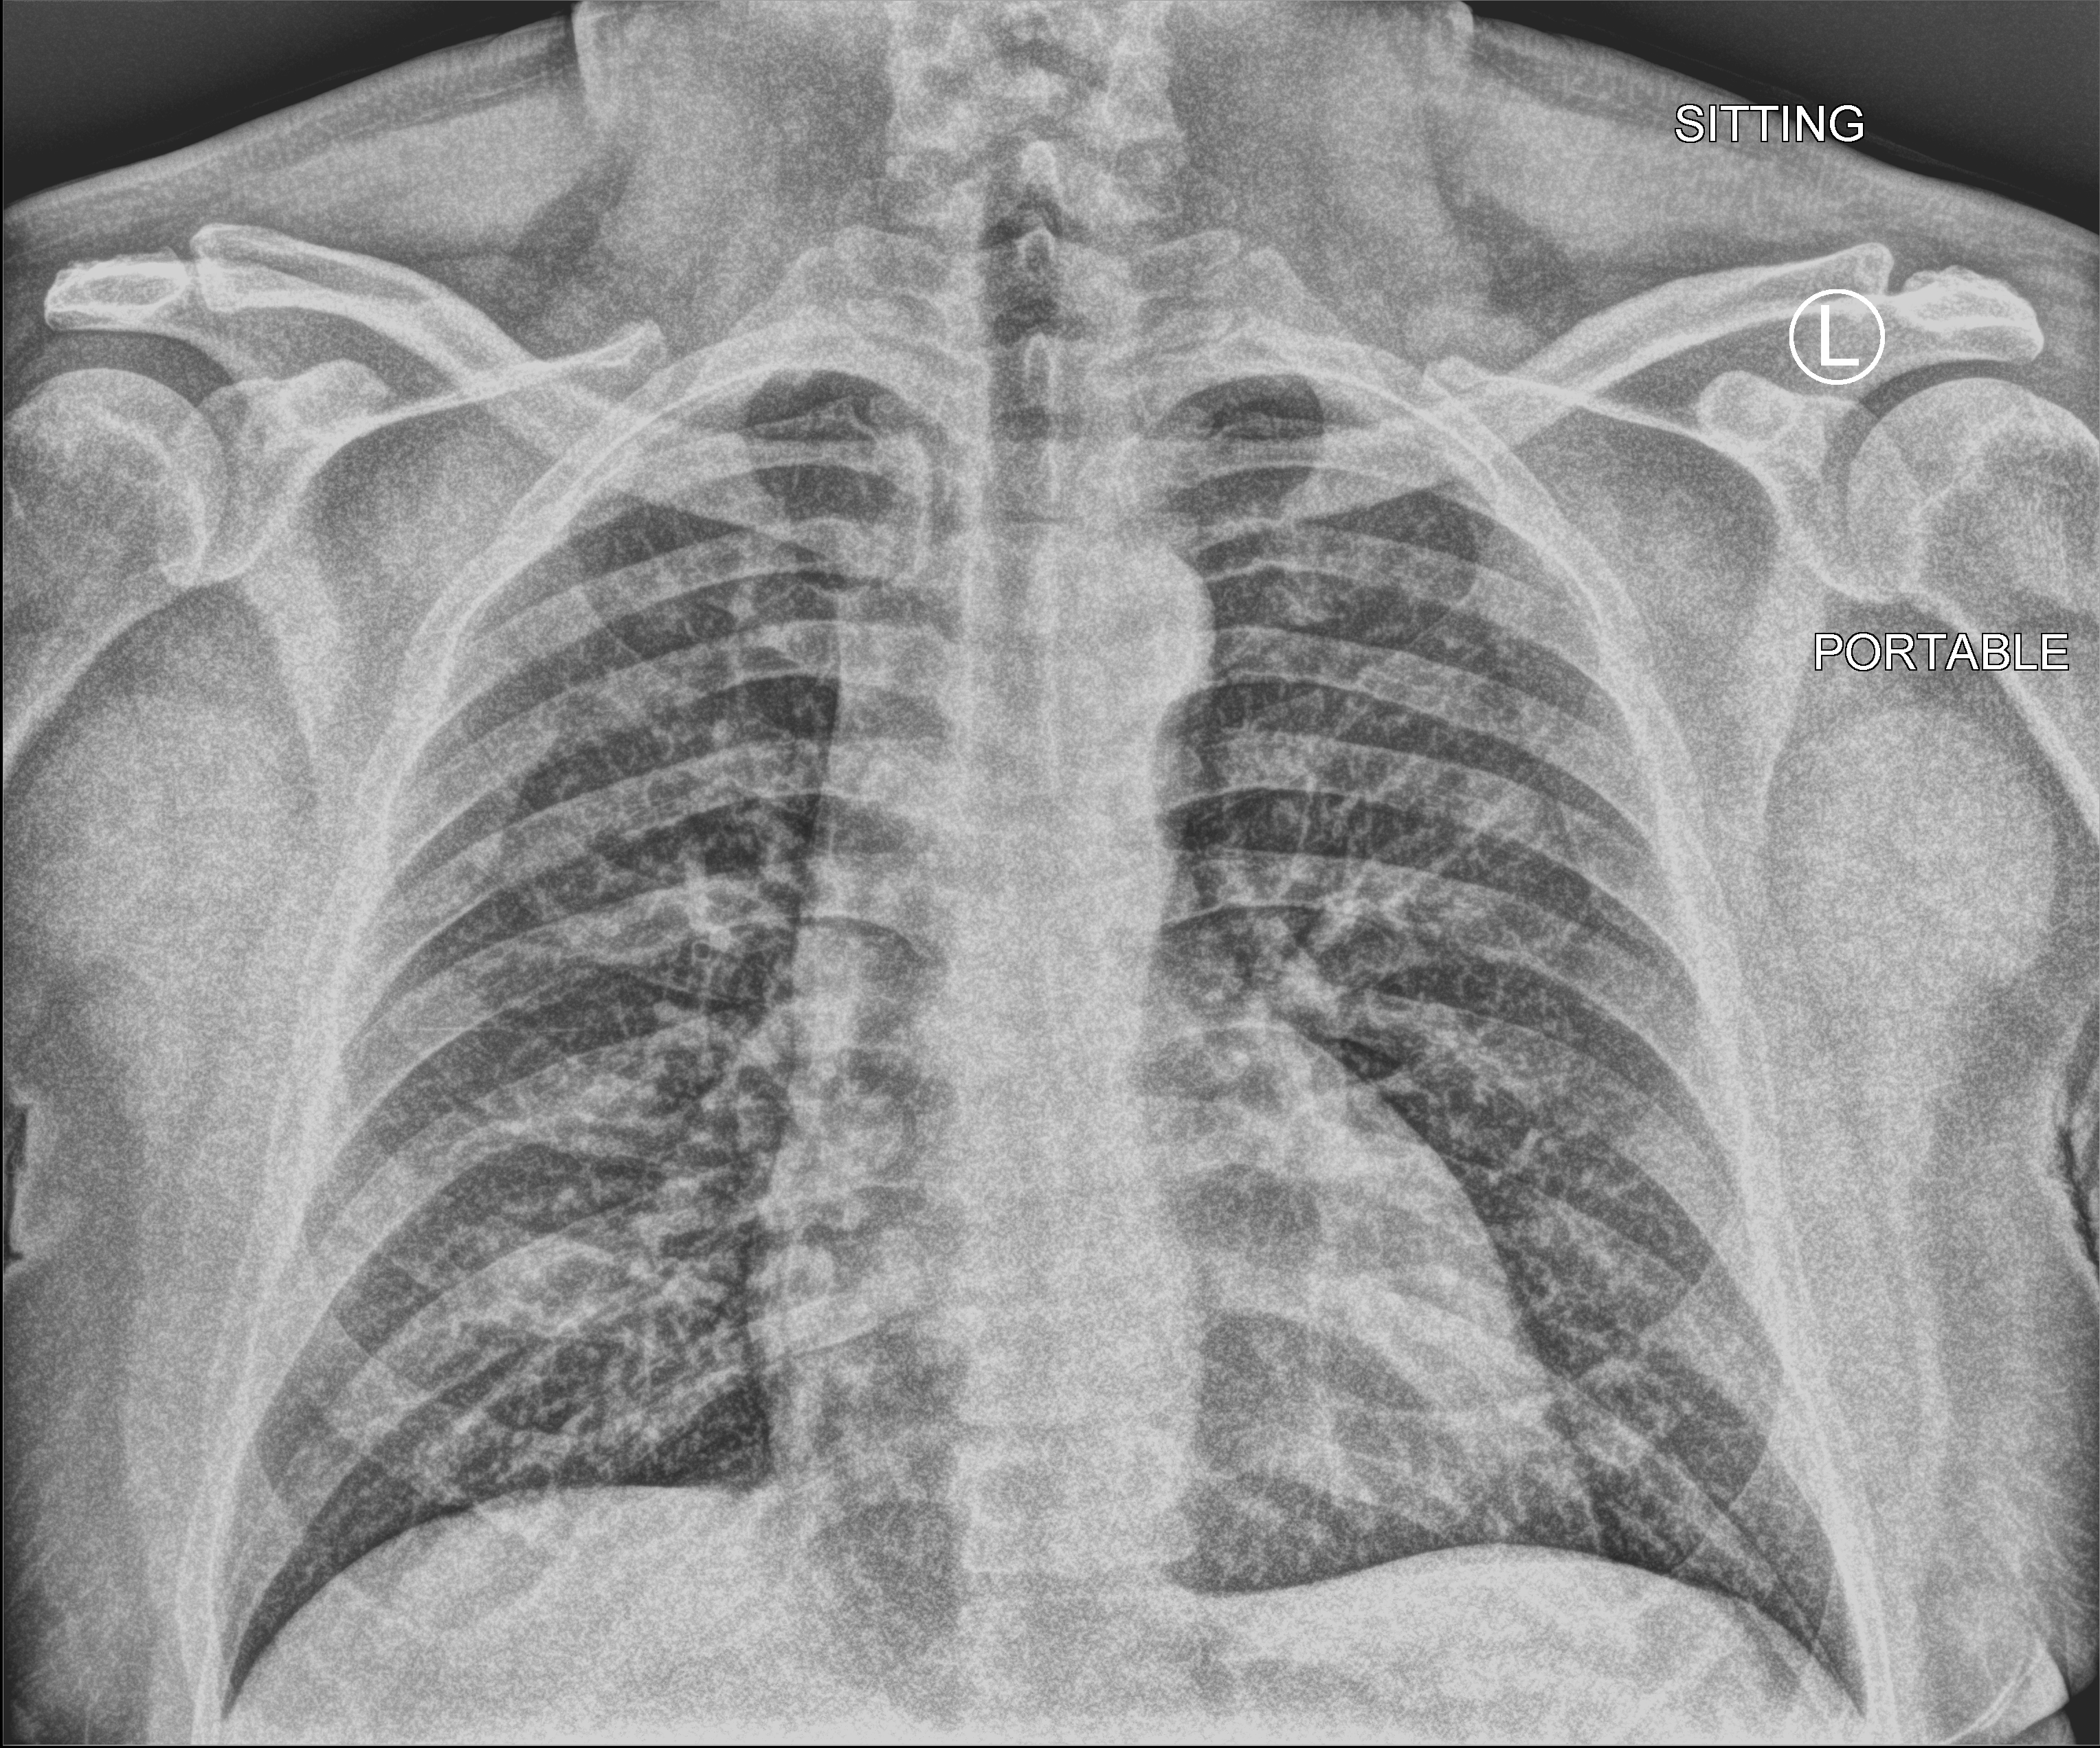
Bedside chest radiograph (computed radiography); anteroposterior (AP) projection. Male patient hospitalised with COVID-19, age 18–59 years.
Admission-level facts for this patient (not findings on this image; timing relative to this image not recorded): admitted to intensive care during this hospital stay: no; mechanically ventilated during this hospital stay: no; COPD (admission record): no.